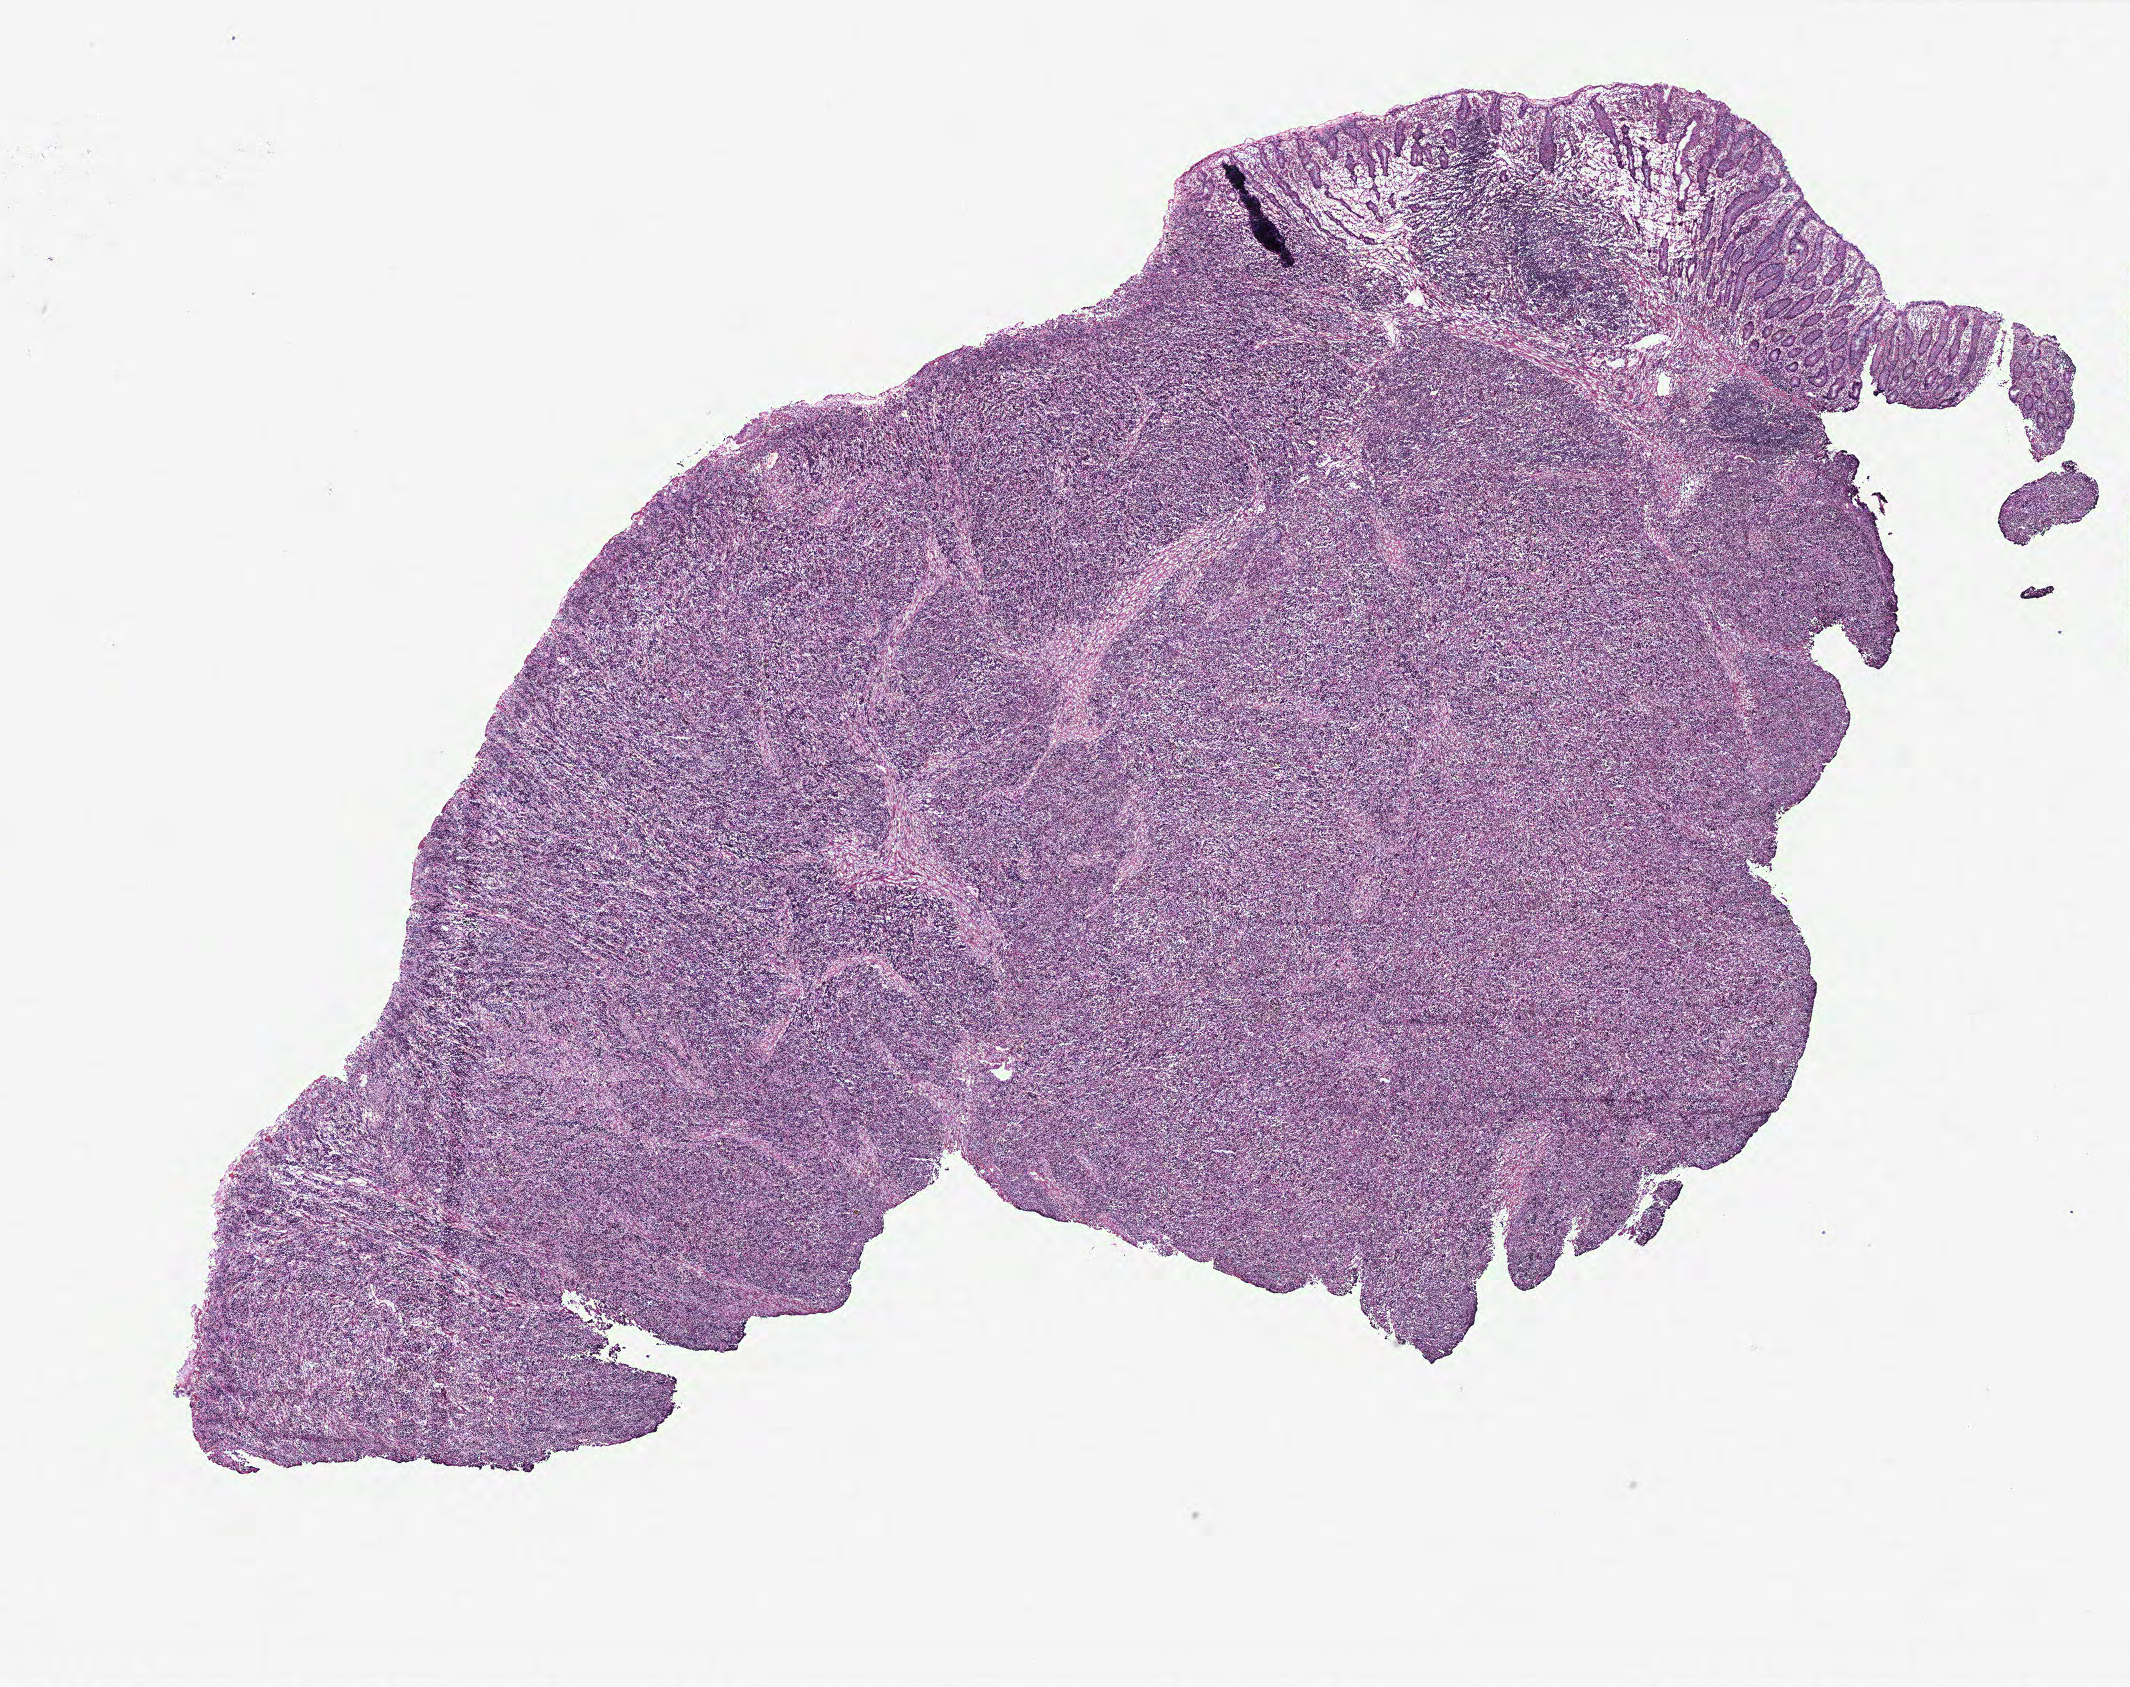
Whole-slide histology image, H&E-stained — whole scanned area (about 17.0 x 13.5 mm) shown as a low-resolution overview. Colon, tissue type not recorded.
- patient diagnosis (cohort enrolment): colon cancer (colon)